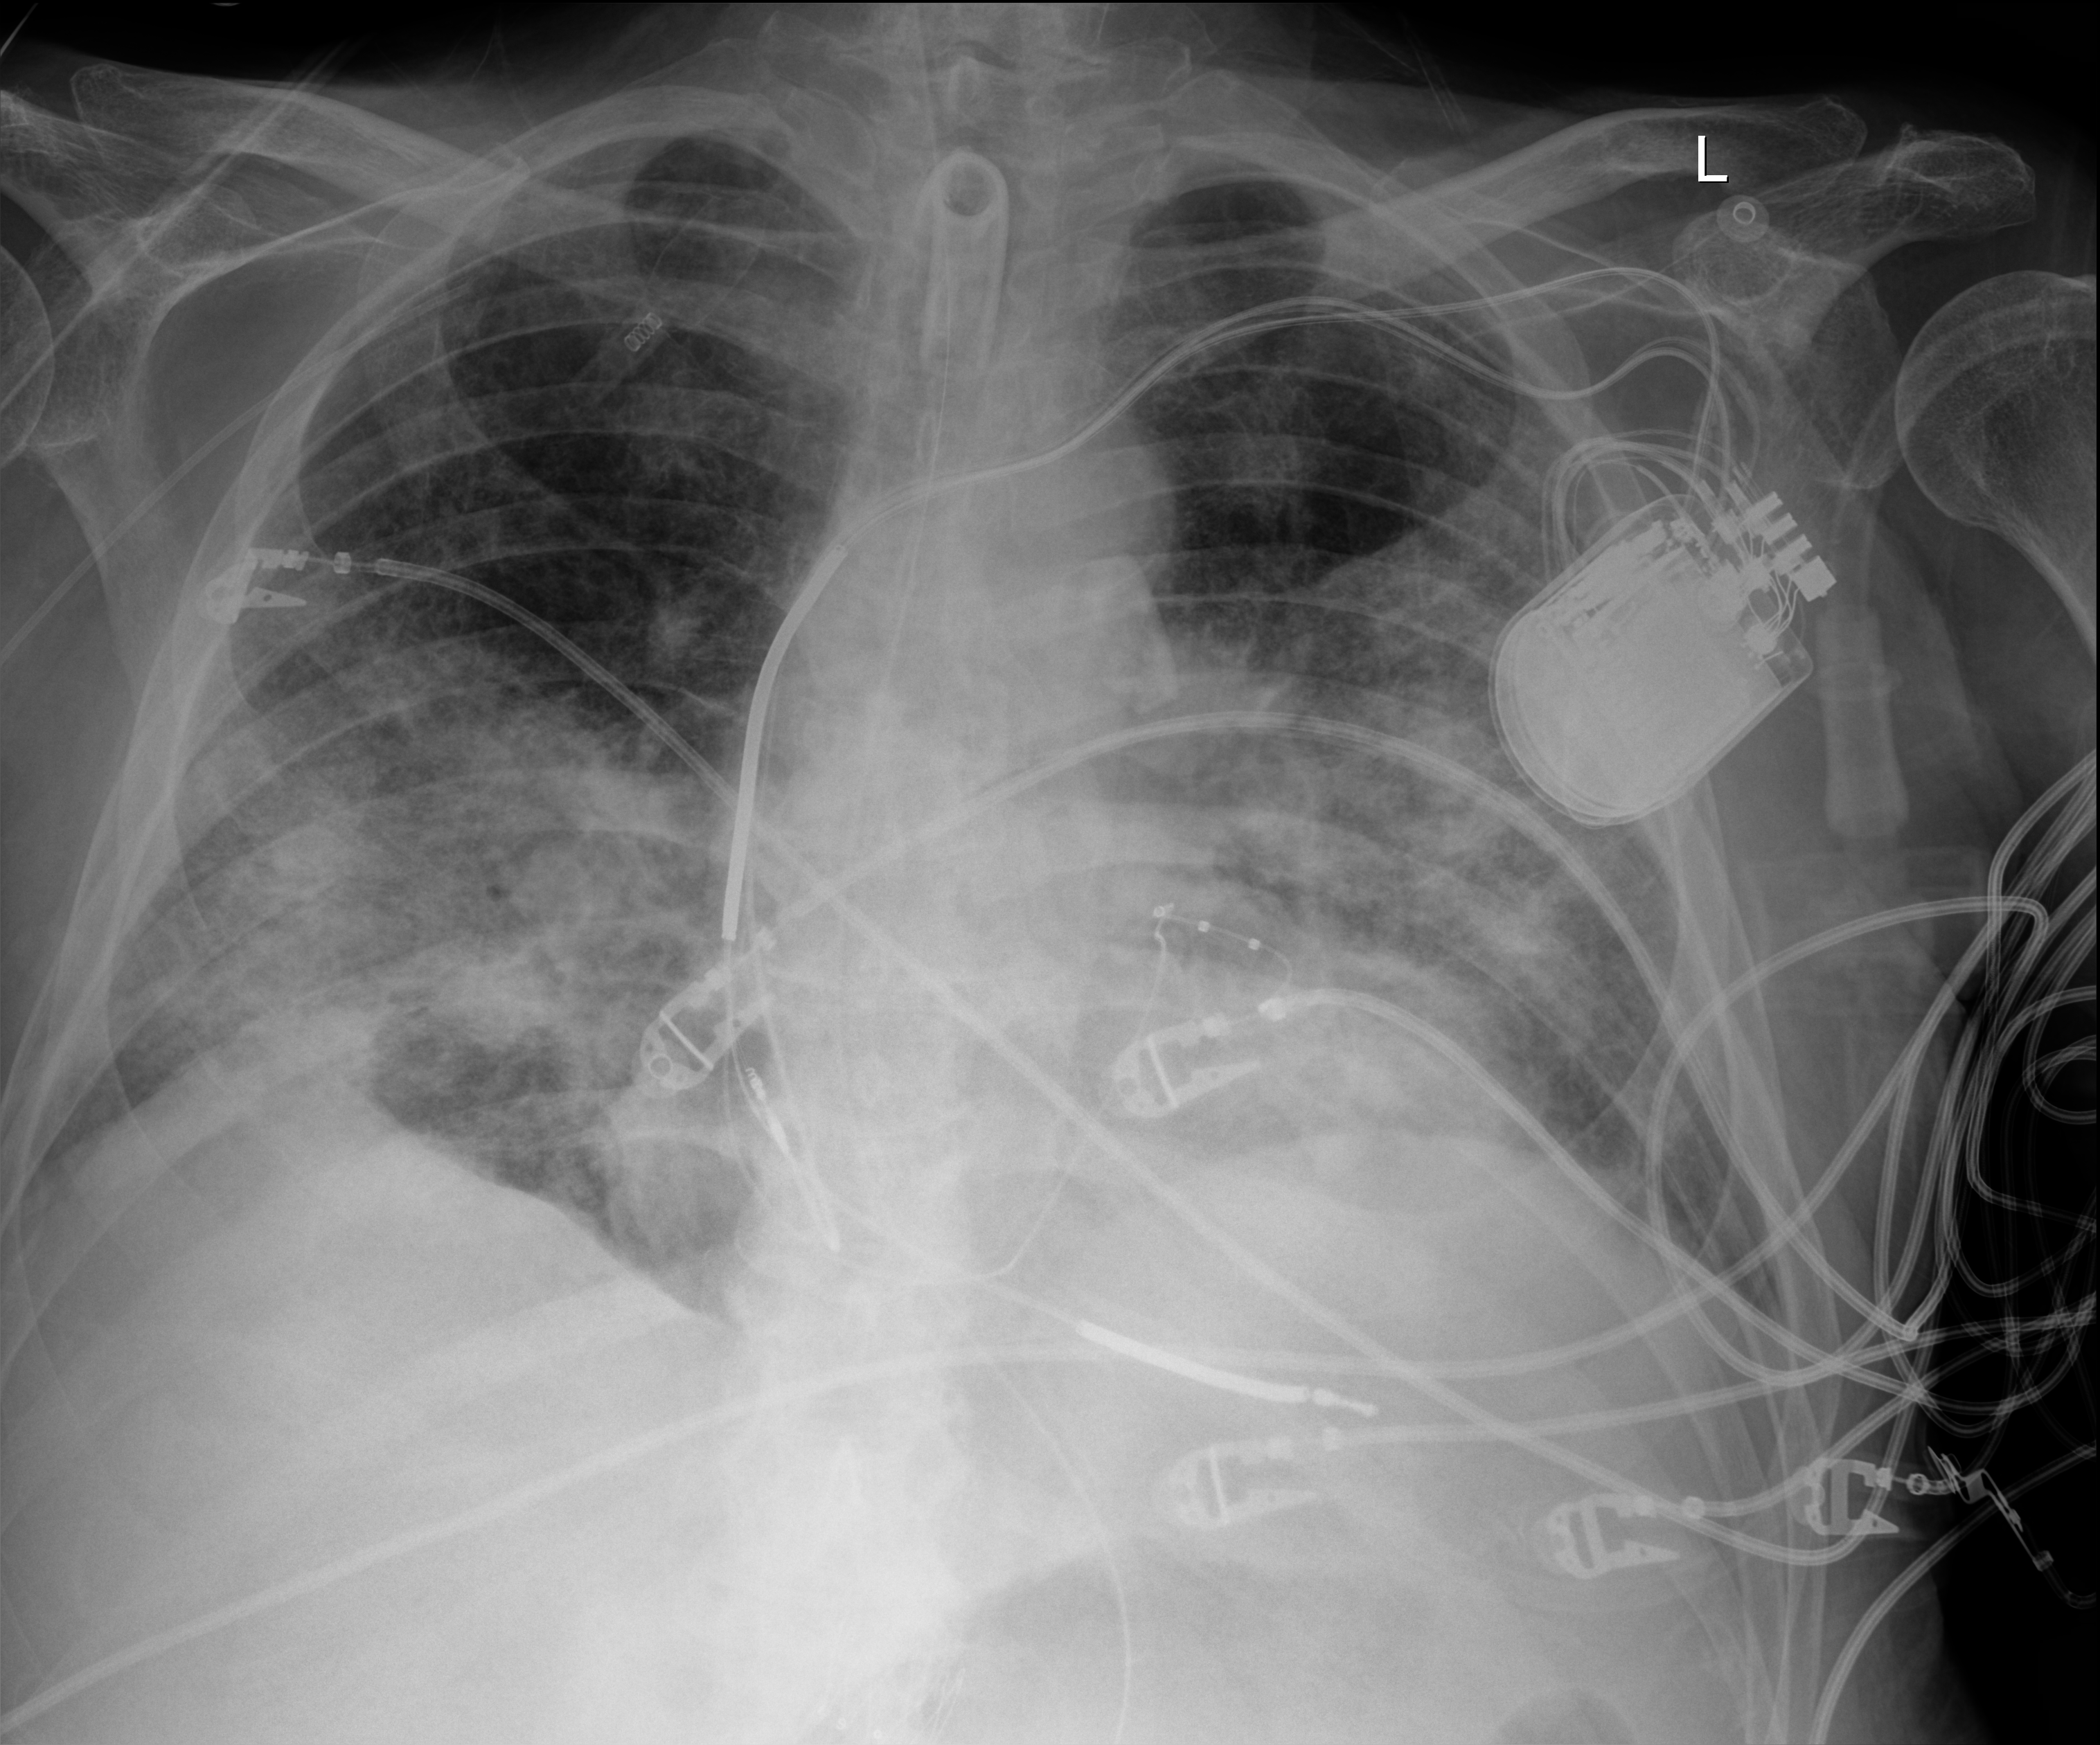
Chest X-ray (portable); anteroposterior (AP) projection. Patient hospitalised with COVID-19; male, aged 60–74 years.
Hospital-stay facts (about this admission, not read from this image; timing relative to this image not recorded):
- length of hospital stay: 36 days